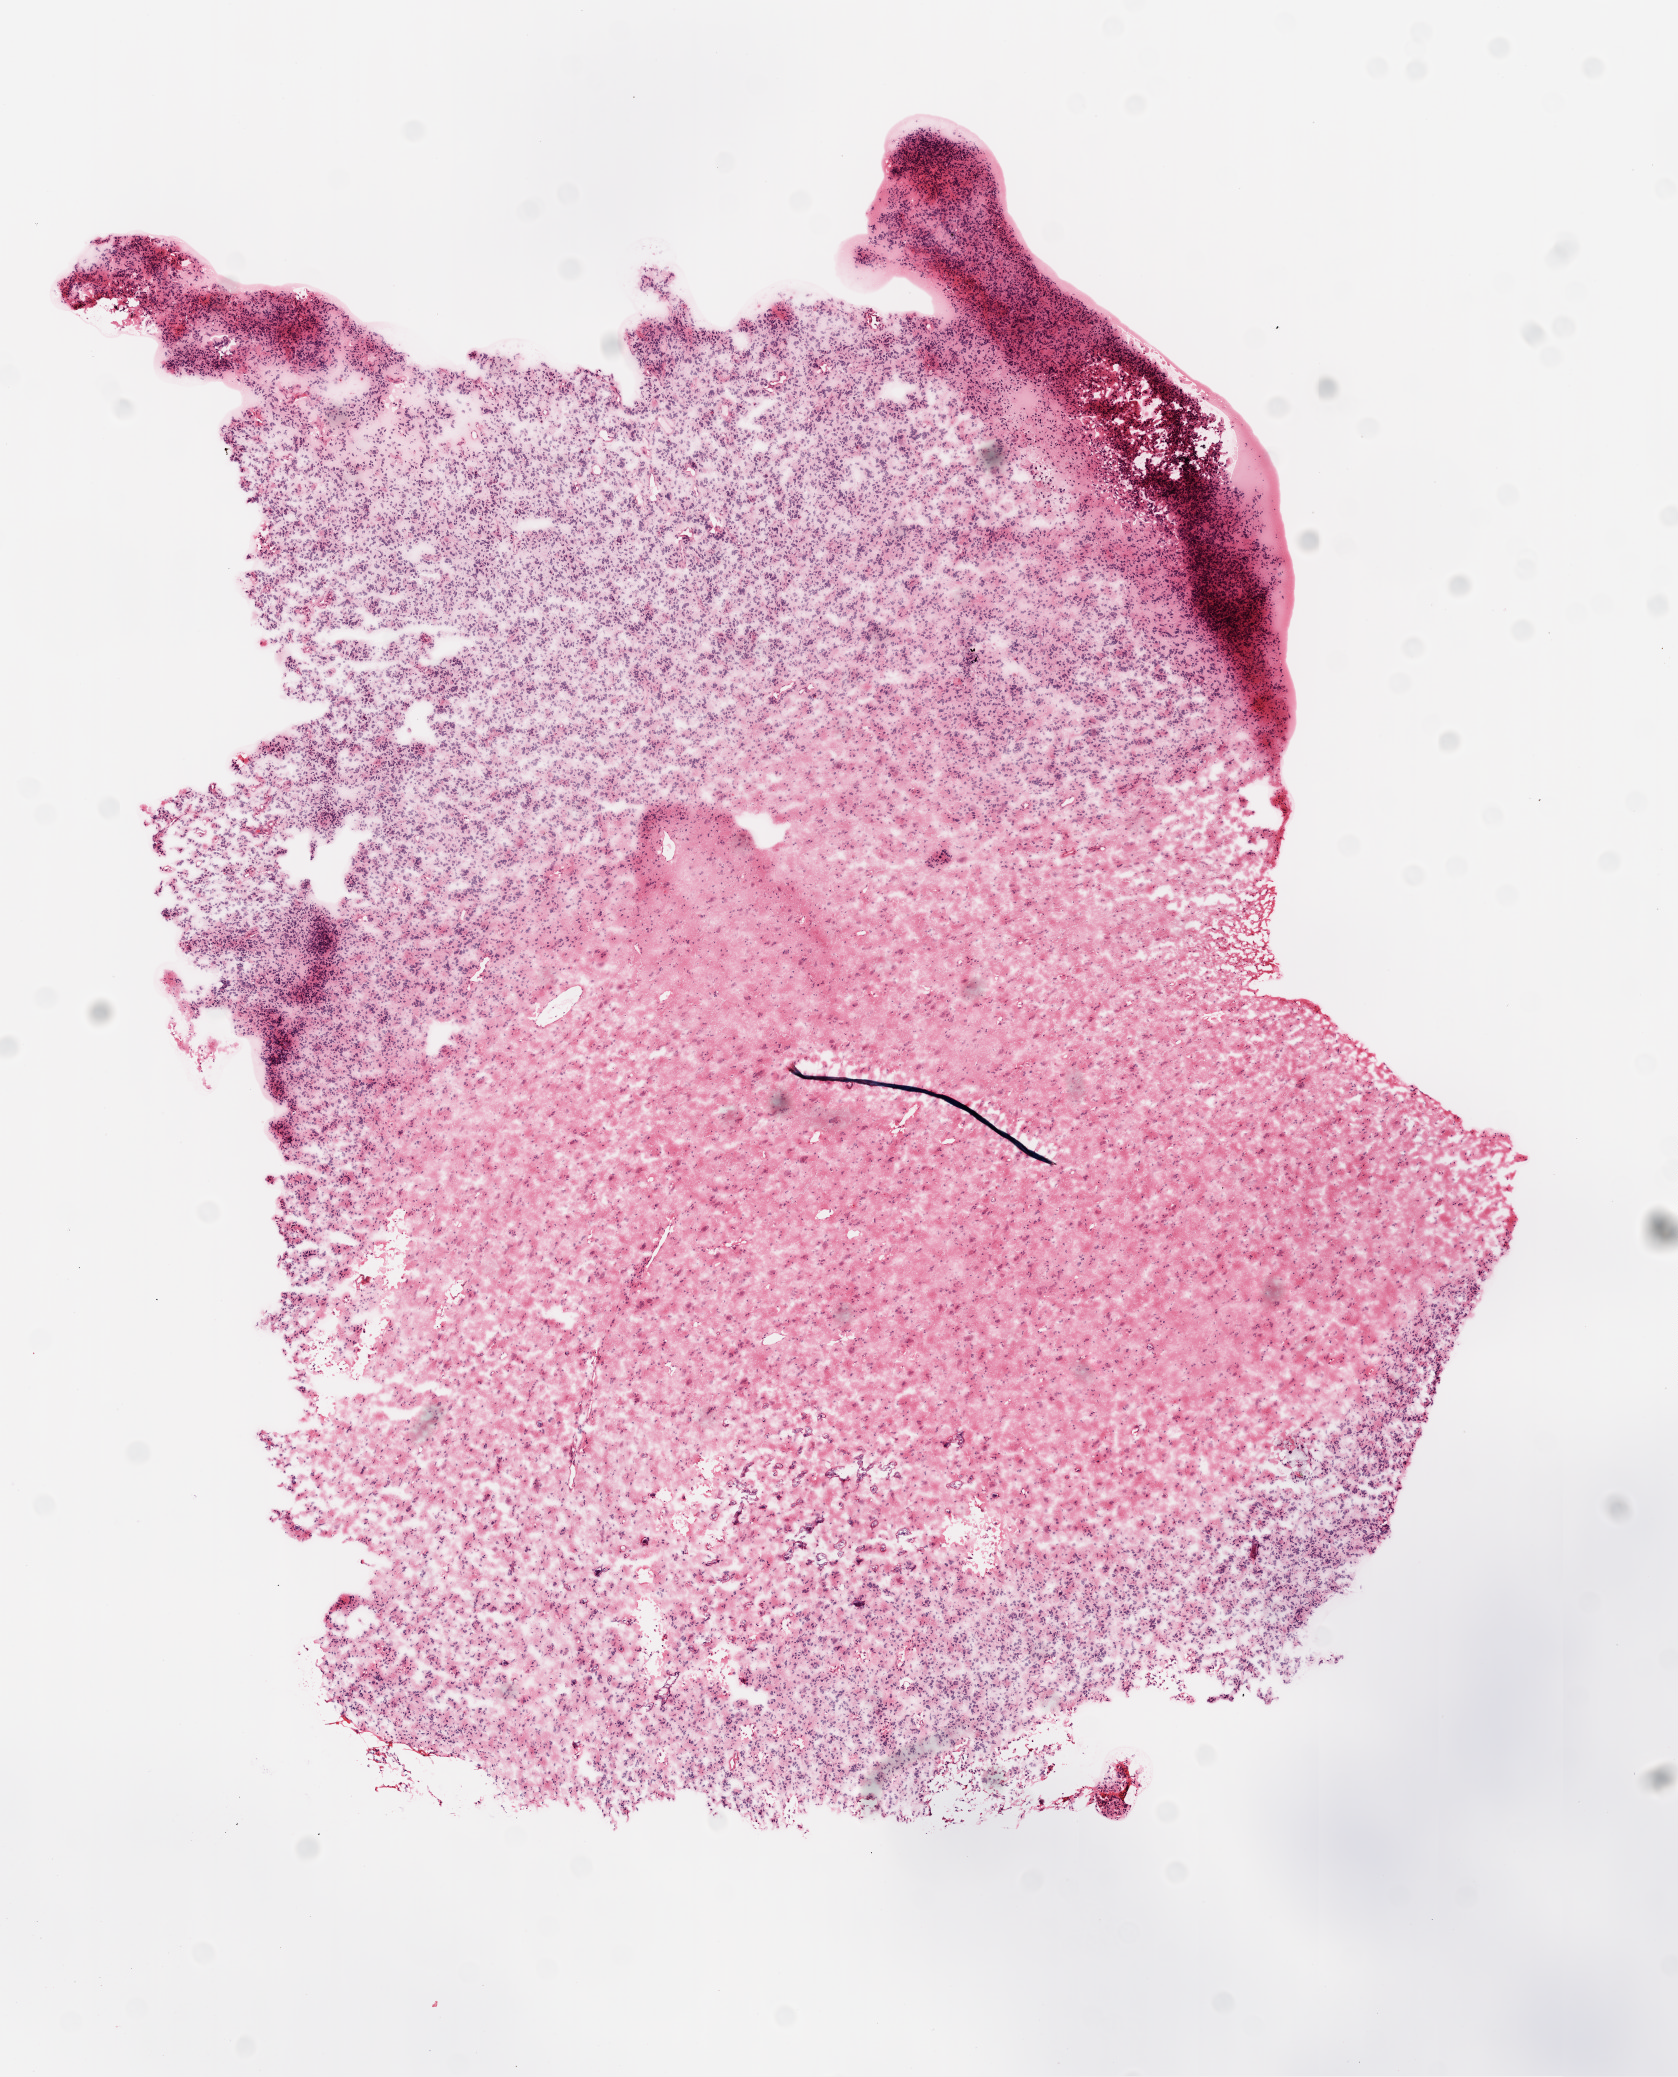
Digitized H&E tissue section (whole slide) — whole scanned area (about 6.8 x 8.4 mm) shown as a low-resolution overview. Frozen section. Primary tumour sample from the brain. Male, age 66 years at initial diagnosis. Slide review estimates, as recorded: tumour cells 60%, tumour nuclei 80%, normal cells 20%, stromal cells 20%, necrosis 0%.
Histologic diagnosis: Glioblastoma.